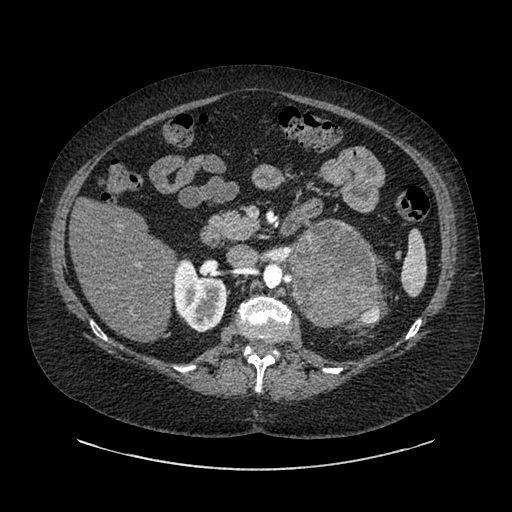
Contrast-enhanced abdominal CT, one axial slice. Position 535 of 769 along the scan axis. 120 kVp. Intravenous contrast given. Soft-tissue window (W 400 / L 40 HU). 0.62 mm slice thickness. 512 × 512 image matrix, field of view 460 × 460 mm. Female patient, age 61 years. Case-level facts recorded for this patient, not image findings: diagnosis: adrenocortical carcinoma; tumour side: left adrenal; tumour size at pathology: 13 cm; Ki-67 index: 79 %; stage (as recorded): 2.
Outlined on this slice (semi-automatic segmentation, software-assisted and operator-edited):
- mass: bounding box [x1, y1, x2, y2] px = [292, 223, 374, 326]